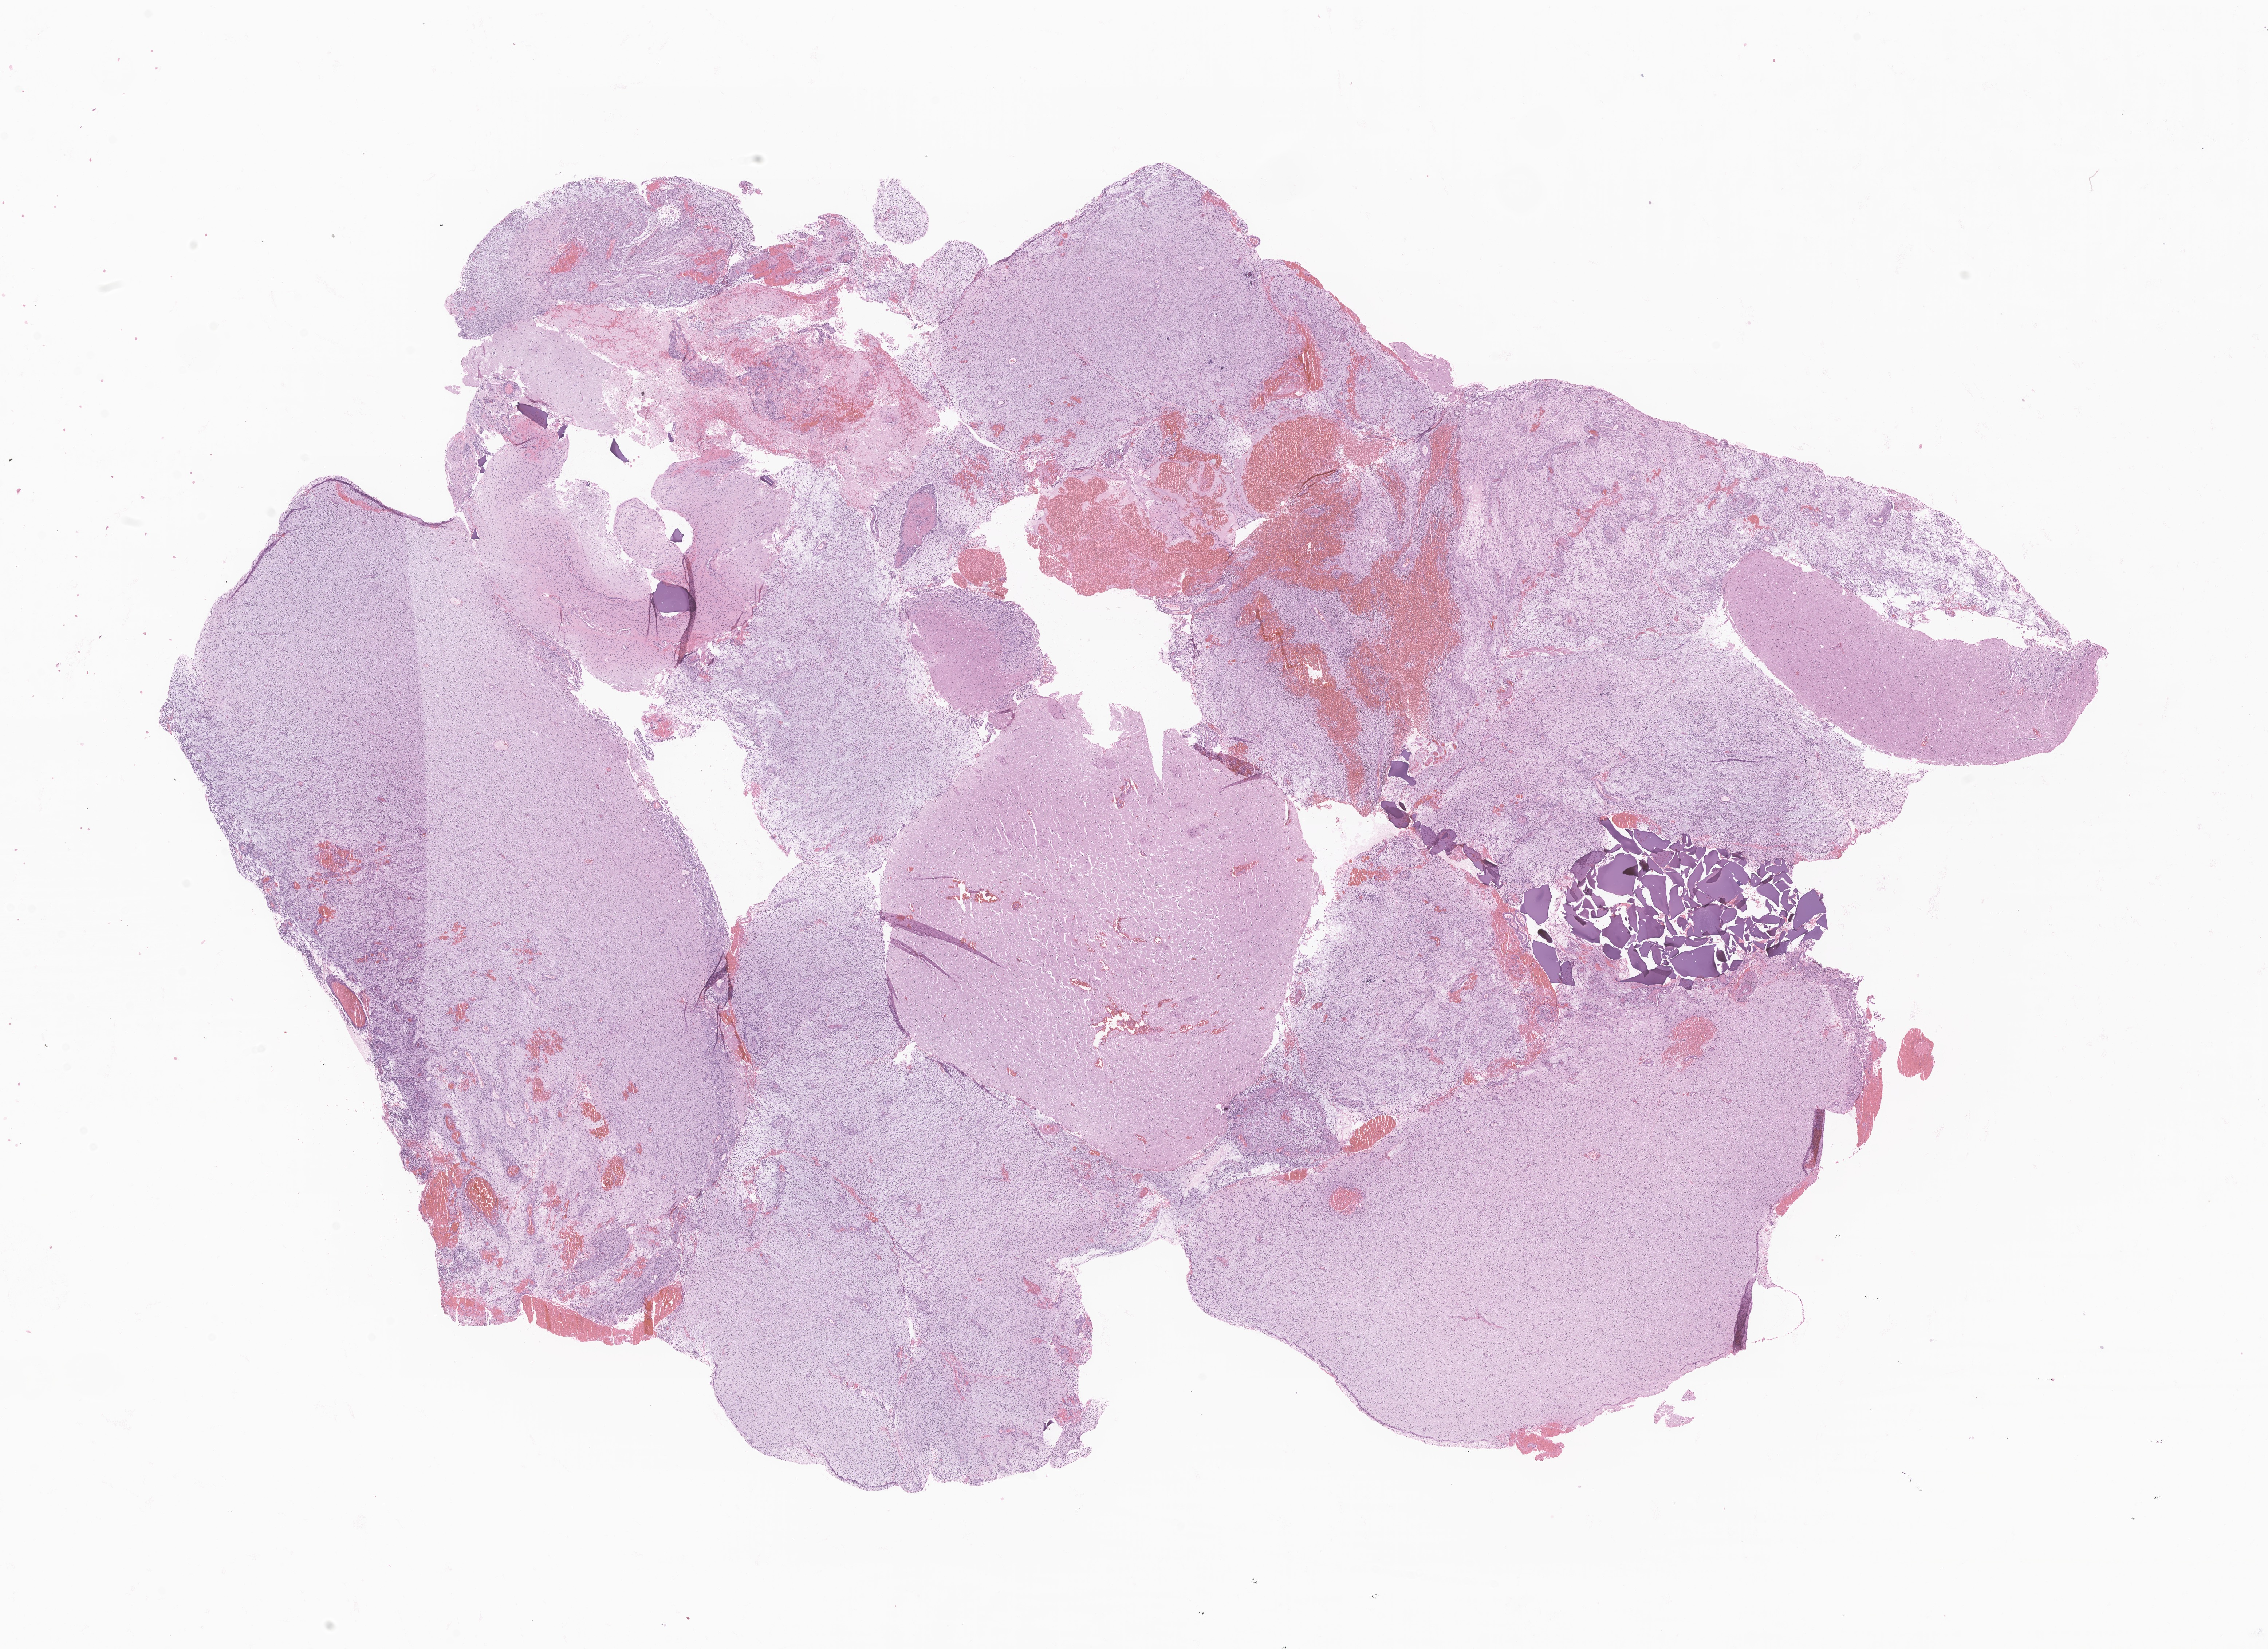
Digitized haematoxylin and eosin-stained section of tumor tissue from the cerebrum, a low-resolution overview of the entire scanned area, about 26.3 x 19.1 mm, formalin-fixed, paraffin-embedded (FFPE) tissue. Patient: female, age 47 months (3 years 11 months).
Diagnosis: Pilocytic astrocytoma.